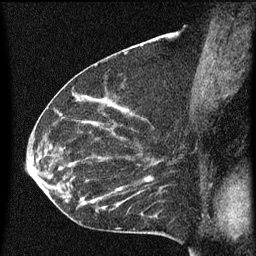
Breast MRI (dynamic contrast-enhanced), one sagittal slice. Dynamic contrast-enhanced series, image 2 of 3 at this slice position (ordered by acquisition). 1.5 T. TE 4.2 ms, TR 8 ms. 2 mm slice thickness. 256 × 256 image matrix. Female patient, age 55 years.
Structures marked on this image (semi-automatic segmentation, software-assisted and operator-edited):
- analysis volume of interest (the breast-tissue region the enhancement analysis was run in; not a lesion): bounding box <51,156,145,217> (left, top, right, bottom; pixels)
- tumour enhancement mask (voxels above the 70 % enhancement threshold inside the analysis volume of interest): <53,166,133,211>